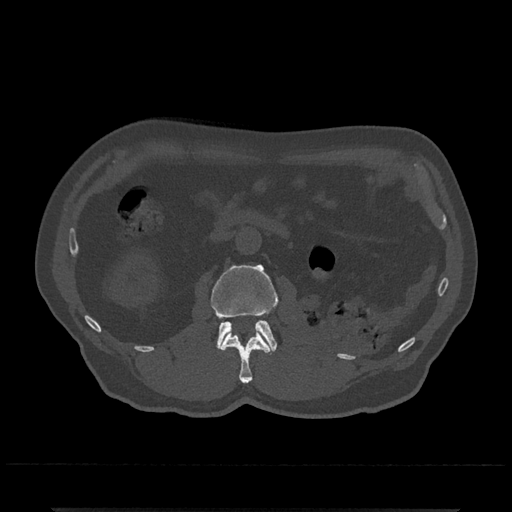
CT including the spine, one axial slice; reconstruction kernel Br40s/3; 120 kVp; bone window (W 1800 / L 400 HU); 0.5 mm slice thickness; 512 × 512 image matrix, field of view 393 × 393 mm. Male patient, age 67 years. Case-level facts recorded for this patient, not image findings: primary cancer: prostate.
Structures marked on this image (semi-automatically segmented with operator editing):
- L1 vertebra: bounding box <220,331,270,383> (left, top, right, bottom; pixels)
- L2 vertebra: <210,264,278,353>